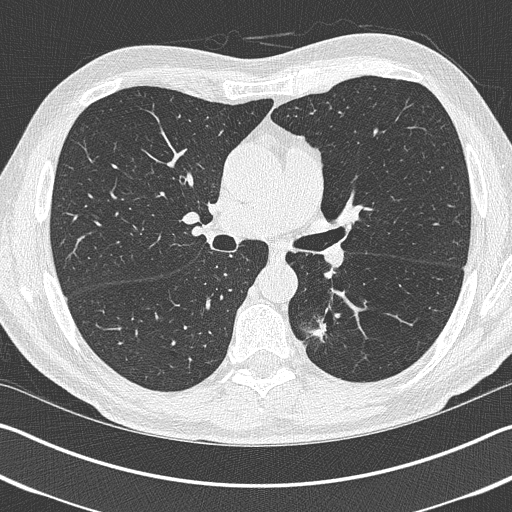
Axial slice from a low-dose chest CT screening exam, first (baseline) screen, lung window (W 1500 / L -600 HU), 1 mm slice thickness, 512 × 512 image matrix. Male, age 69 years at enrolment.
Expert-annotated lung lesion, bounding box [x1, y1, x2, y2] px = [300, 308, 355, 360]. Reader record for this screening exam (exam-level; its link to the box is not recorded): non-calcified nodule or mass ≥4 mm, left upper lobe, 19 × 19 mm, spiculated (stellate) margins, pre-existing on the prior screen: yes. Official screen result: positive, change unspecified: nodule(s) >= 4 mm or enlarging nodule(s), mass(es), or other non-specific abnormalities suspicious for lung cancer. Later outcome: lung cancer diagnosed 202 days after this screen — non-small cell carcinoma, left lower lobe, stage IIIA (AJCC 6th edition), 20 mm at pathology.